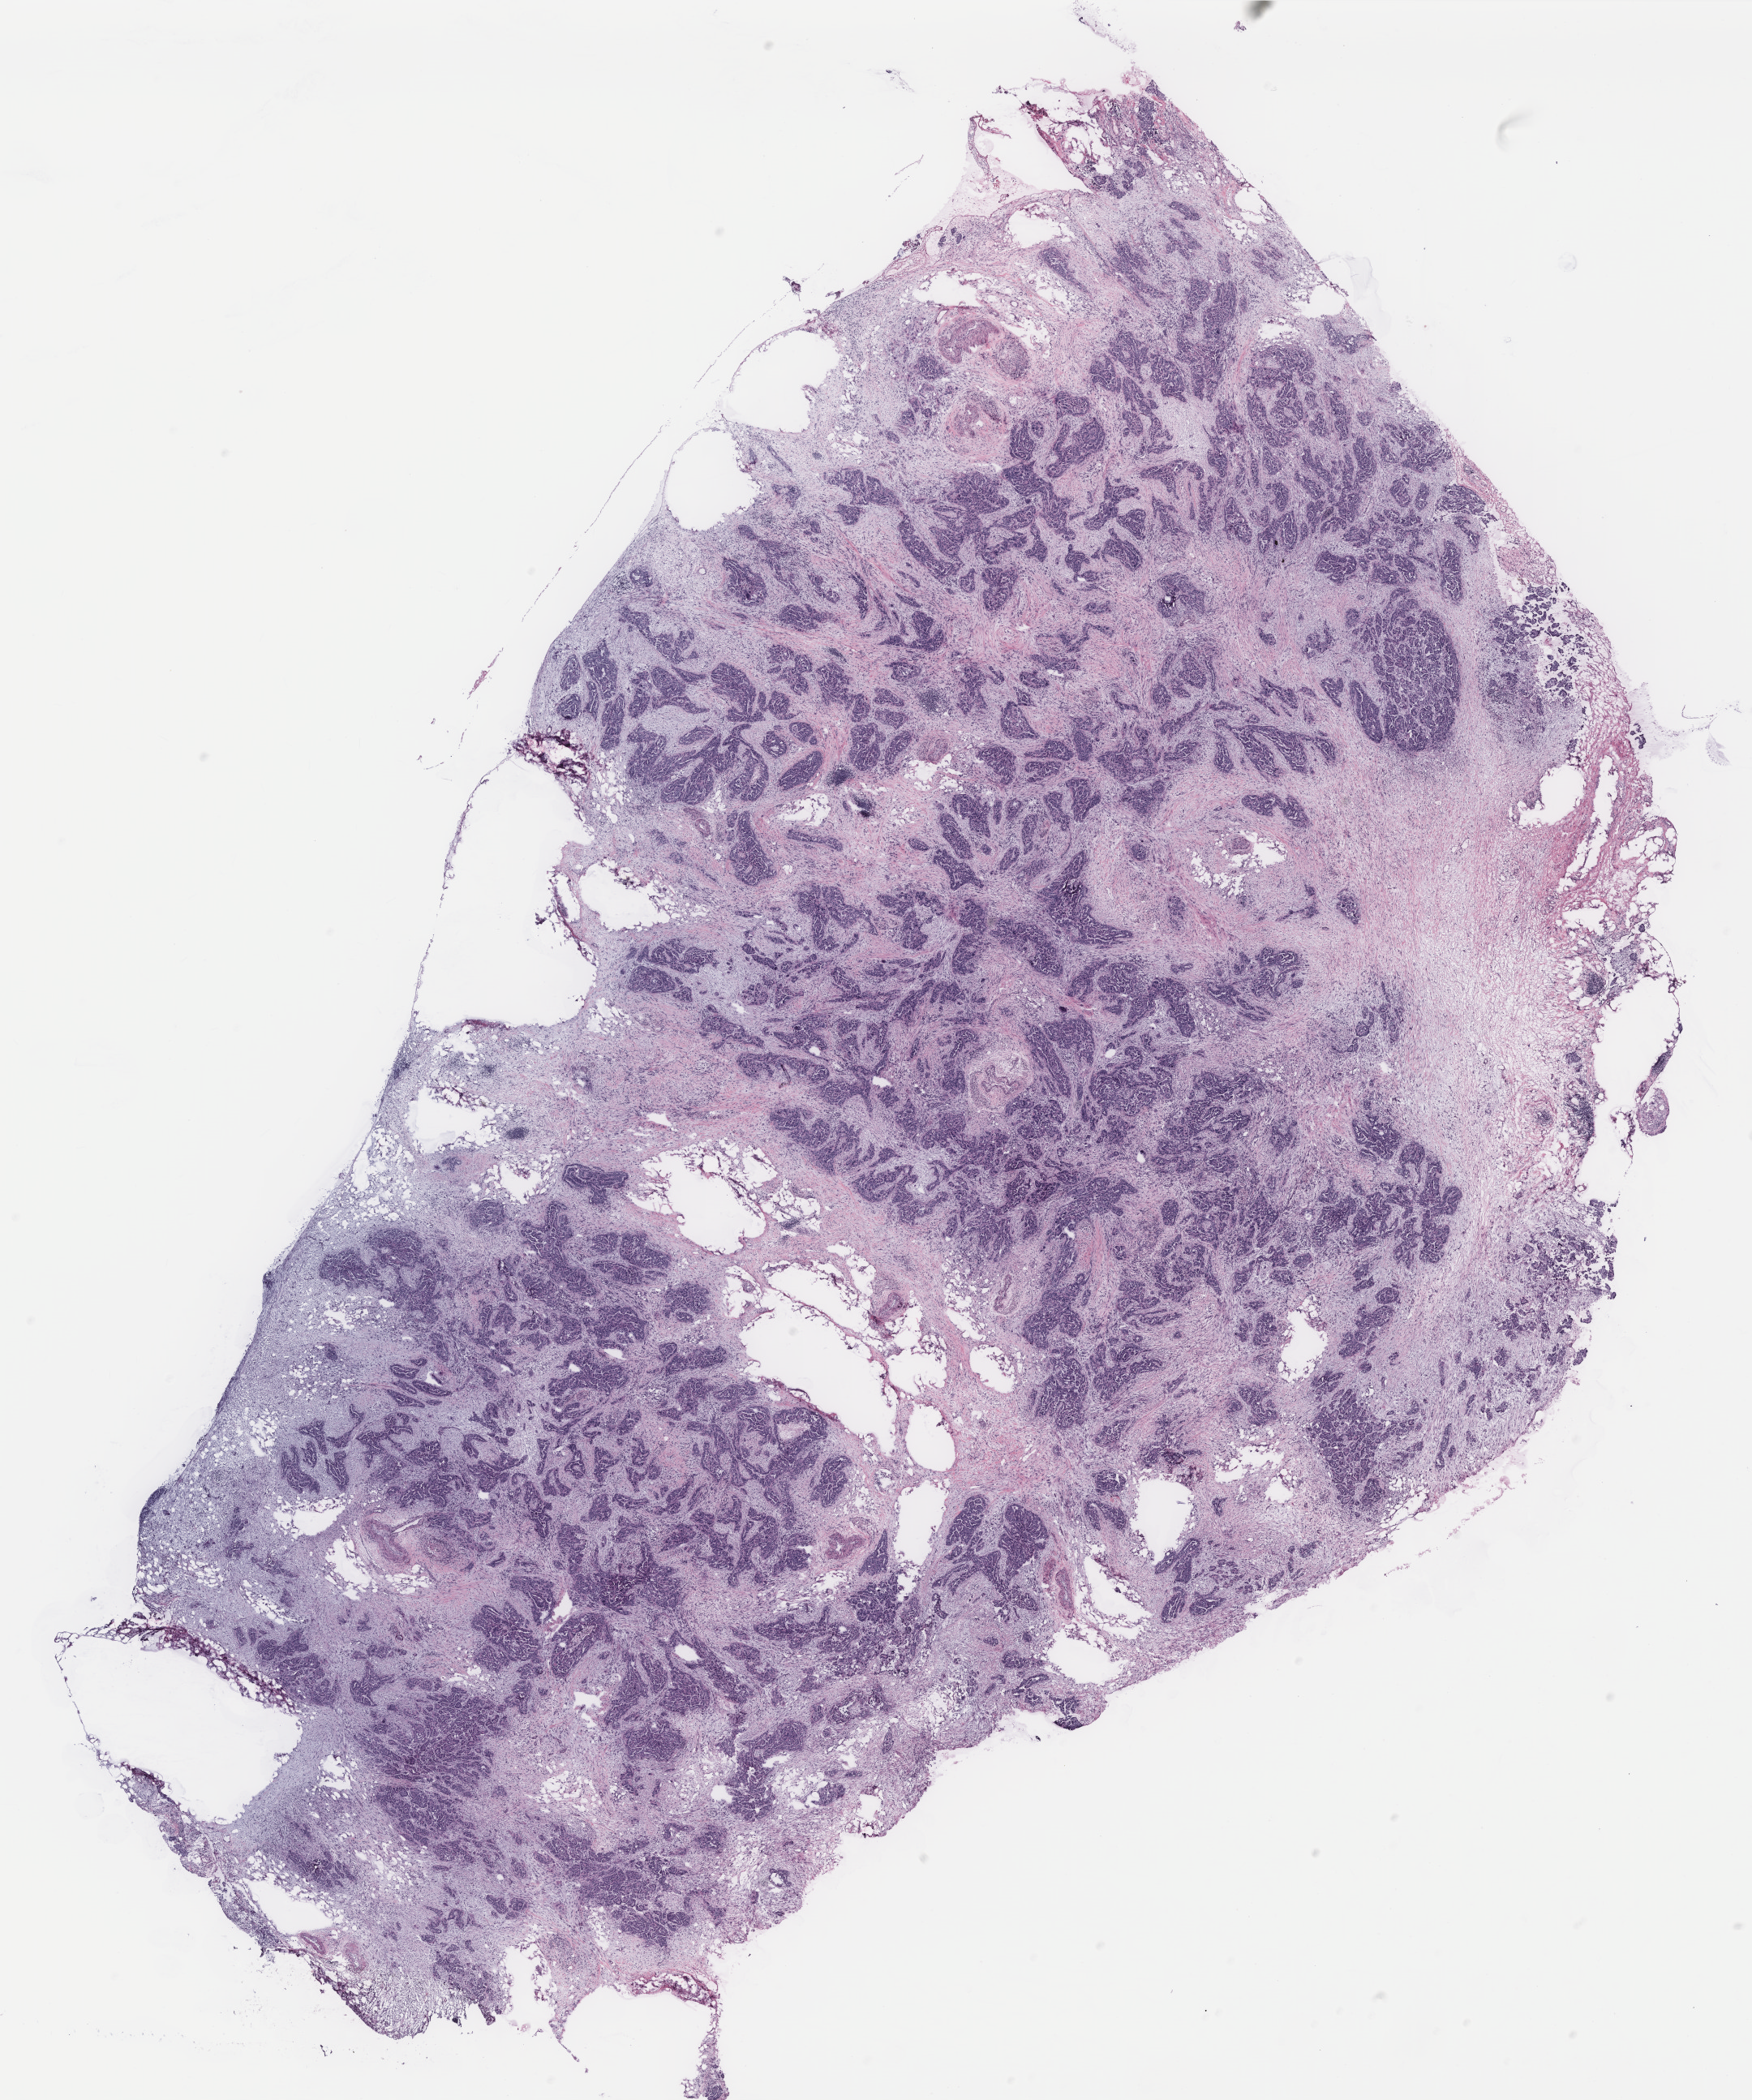
Digitized Hematoxylin and eosin (H&E) stained tissue section (whole slide), shown as a low-resolution overview of the whole scanned area (about 17.3 x 20.7 mm); tumour tissue sample, ovary. Female, 72 y/o.
Diagnosis: Serous adenocarcinoma, NOS (fallopian tube).